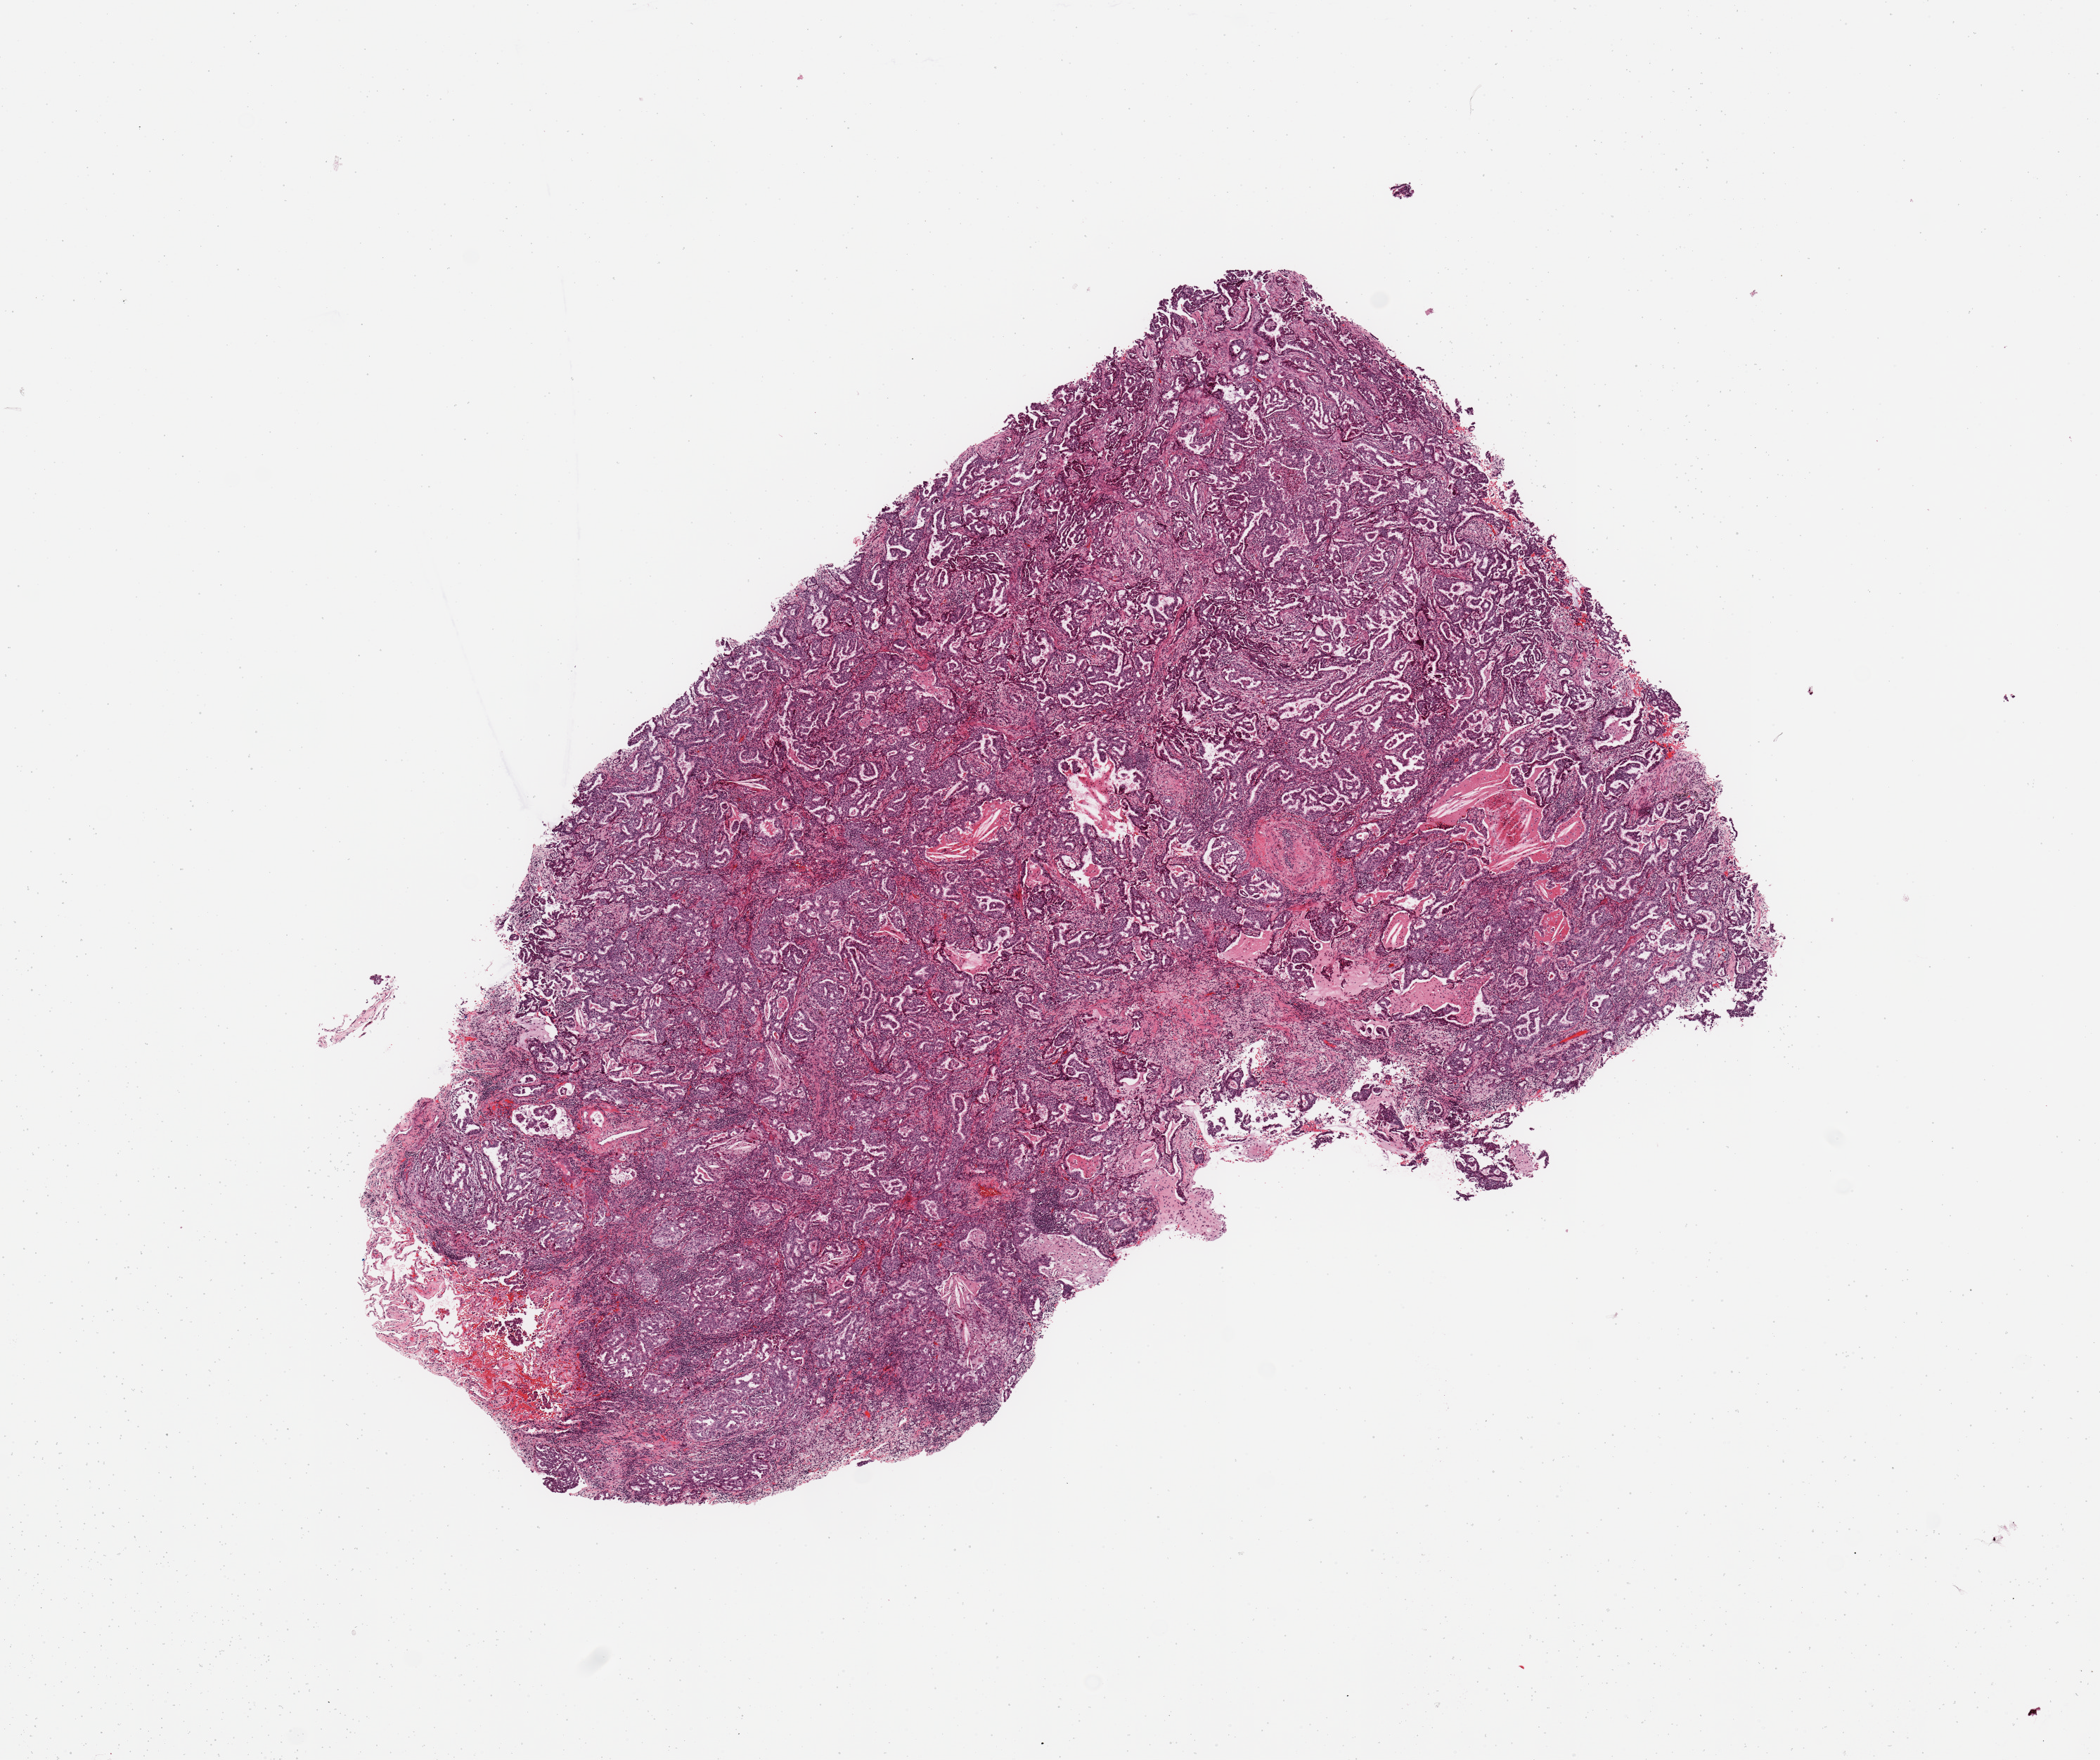
Whole-slide histology image, H&E-stained, shown as a low-resolution overview of the whole scanned area (about 11.8 x 9.9 mm, acquisition: 20x scan); lung, tumour tissue. 61-year-old female patient. Histologic grade: G2 (moderately differentiated).
AJCC pathologic stage: IIIA. Diagnosis: Adenocarcinoma, NOS. Primary tumour site (as recorded): right upper lobe.